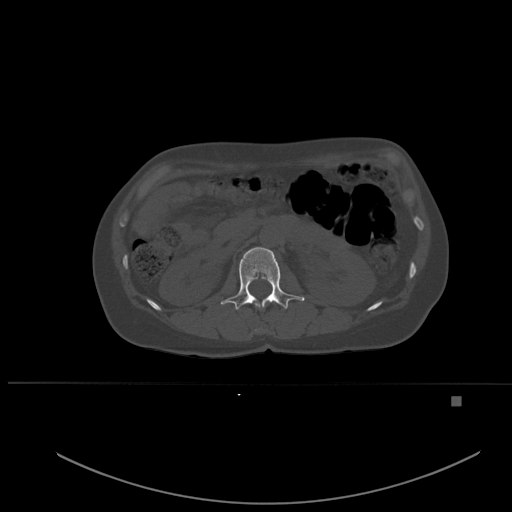
CT including the spine, one axial slice; bone window (W 1800 / L 400 HU); 1.5 mm slice thickness; 512 × 512 image matrix, field of view 443 × 443 mm. Patient: female, 49 years. From the clinical record (not read from this slice): primary cancer: breast; vertebrae with lytic lesions (as recorded): L3, T12, L4.
Structures marked on this image (semi-automatically segmented with operator editing):
- L1 vertebra: bounding box (x1, y1, x2, y2) in pixels: (221, 247, 305, 310)